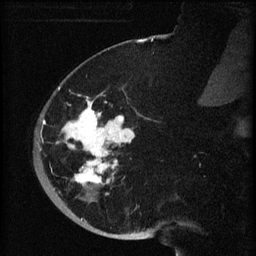
Breast MRI (dynamic contrast-enhanced), one sagittal slice. Position 21 of 60 along the scan axis. Dynamic contrast-enhanced series, image 2 of 3 at this slice position (ordered by acquisition). 1.5 T. TE 4.2 ms, TR 8.2 ms. 2 mm slice thickness. 256 × 256 image matrix. Female patient, age 71 years.
Structures marked on this image (semi-automatically segmented with operator editing):
- analysis volume of interest (the breast-tissue region the enhancement analysis was run in; not a lesion): bounding box <40,72,148,196> (left, top, right, bottom; pixels)
- tumour enhancement mask (voxels above the 70 % enhancement threshold inside the analysis volume of interest): <40,87,135,187>